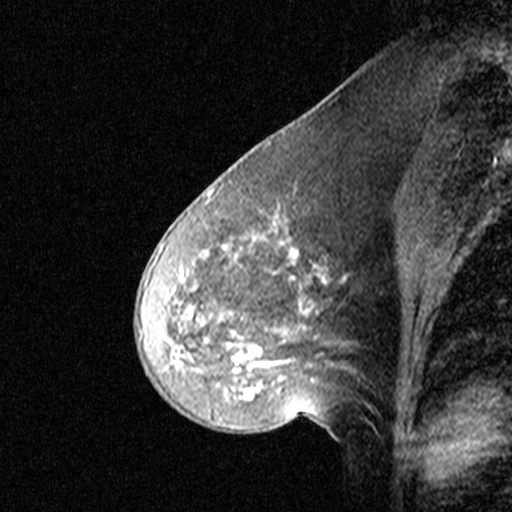
Breast MRI (dynamic contrast-enhanced), one sagittal slice. Slice 18 of 44 in the series (ordered by position). Dynamic contrast-enhanced study with each time point stored as its own series, time point 2 of 3 at this slice position (early post-contrast, ordered by acquisition time). 1.5 T. TE 4.5 ms, TR 11 ms. 3 mm slice thickness. 512 × 512 image matrix. Female patient, age 46 years. From the clinical record (not read from this slice): setting: breast cancer imaged before/during neoadjuvant chemotherapy; receptor status: HER2-positive.
Structures marked on this image (semi-automatic segmentation, software-assisted and operator-edited):
- analysis volume of interest (the breast-tissue region the enhancement analysis was run in; not a lesion): bounding box (x1, y1, x2, y2) in pixels: (144, 172, 359, 393)
- tumour enhancement mask (voxels above the 90 % enhancement threshold inside the analysis volume of interest): (166, 189, 346, 376)